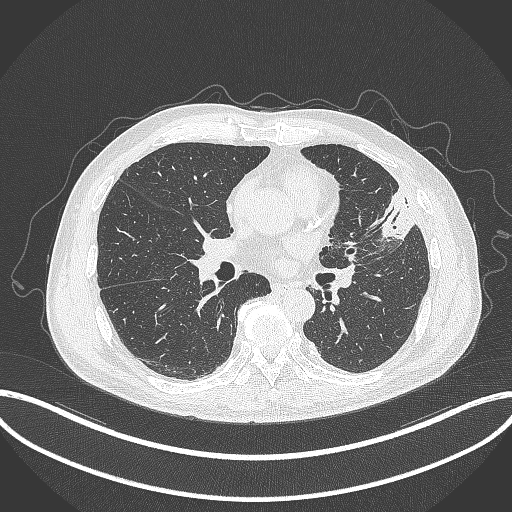
Chest CT, one axial slice. Slice 166 of 382 in the series (ordered by position). Reconstruction kernel B70f. 120 kVp. Lung window (W 1500 / L -600 HU). 1 mm slice thickness. 512 × 512 image matrix, field of view 415 × 415 mm. Male patient, age 64 years. From the clinical record (not read from this slice): clinical TNM (as recorded): T4 N1 M0; histopathological grade: G3.
Outlined on this slice (rectangle marked by the reading radiologist):
- lung tumour (recorded histology: adenocarcinoma): bounding box <369,186,419,244> (left, top, right, bottom; pixels)